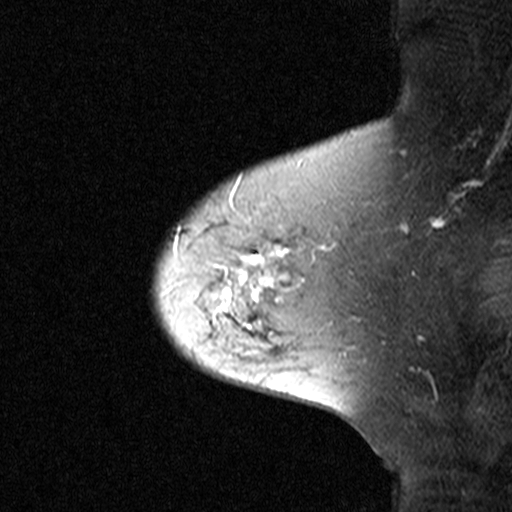
Breast MRI (dynamic contrast-enhanced), one sagittal slice. Position 35 of 44 along the scan axis. Dynamic contrast-enhanced study with each time point stored as its own series, time point 2 of 3 at this slice position (early post-contrast, ordered by acquisition time). 1.5 T. TE 4.5 ms, TR 11 ms. 3 mm slice thickness. 512 × 512 image matrix. Female patient, age 65 years. From the clinical record (not read from this slice): setting: breast cancer imaged before/during neoadjuvant chemotherapy; receptor status: HER2-positive.
Structures marked on this image (semi-automatic segmentation, software-assisted and operator-edited):
- analysis volume of interest (the breast-tissue region the enhancement analysis was run in; not a lesion): bounding box (x1, y1, x2, y2) in pixels: (160, 172, 329, 345)
- tumour enhancement mask (voxels above the 90 % enhancement threshold inside the analysis volume of interest): (221, 174, 288, 330)